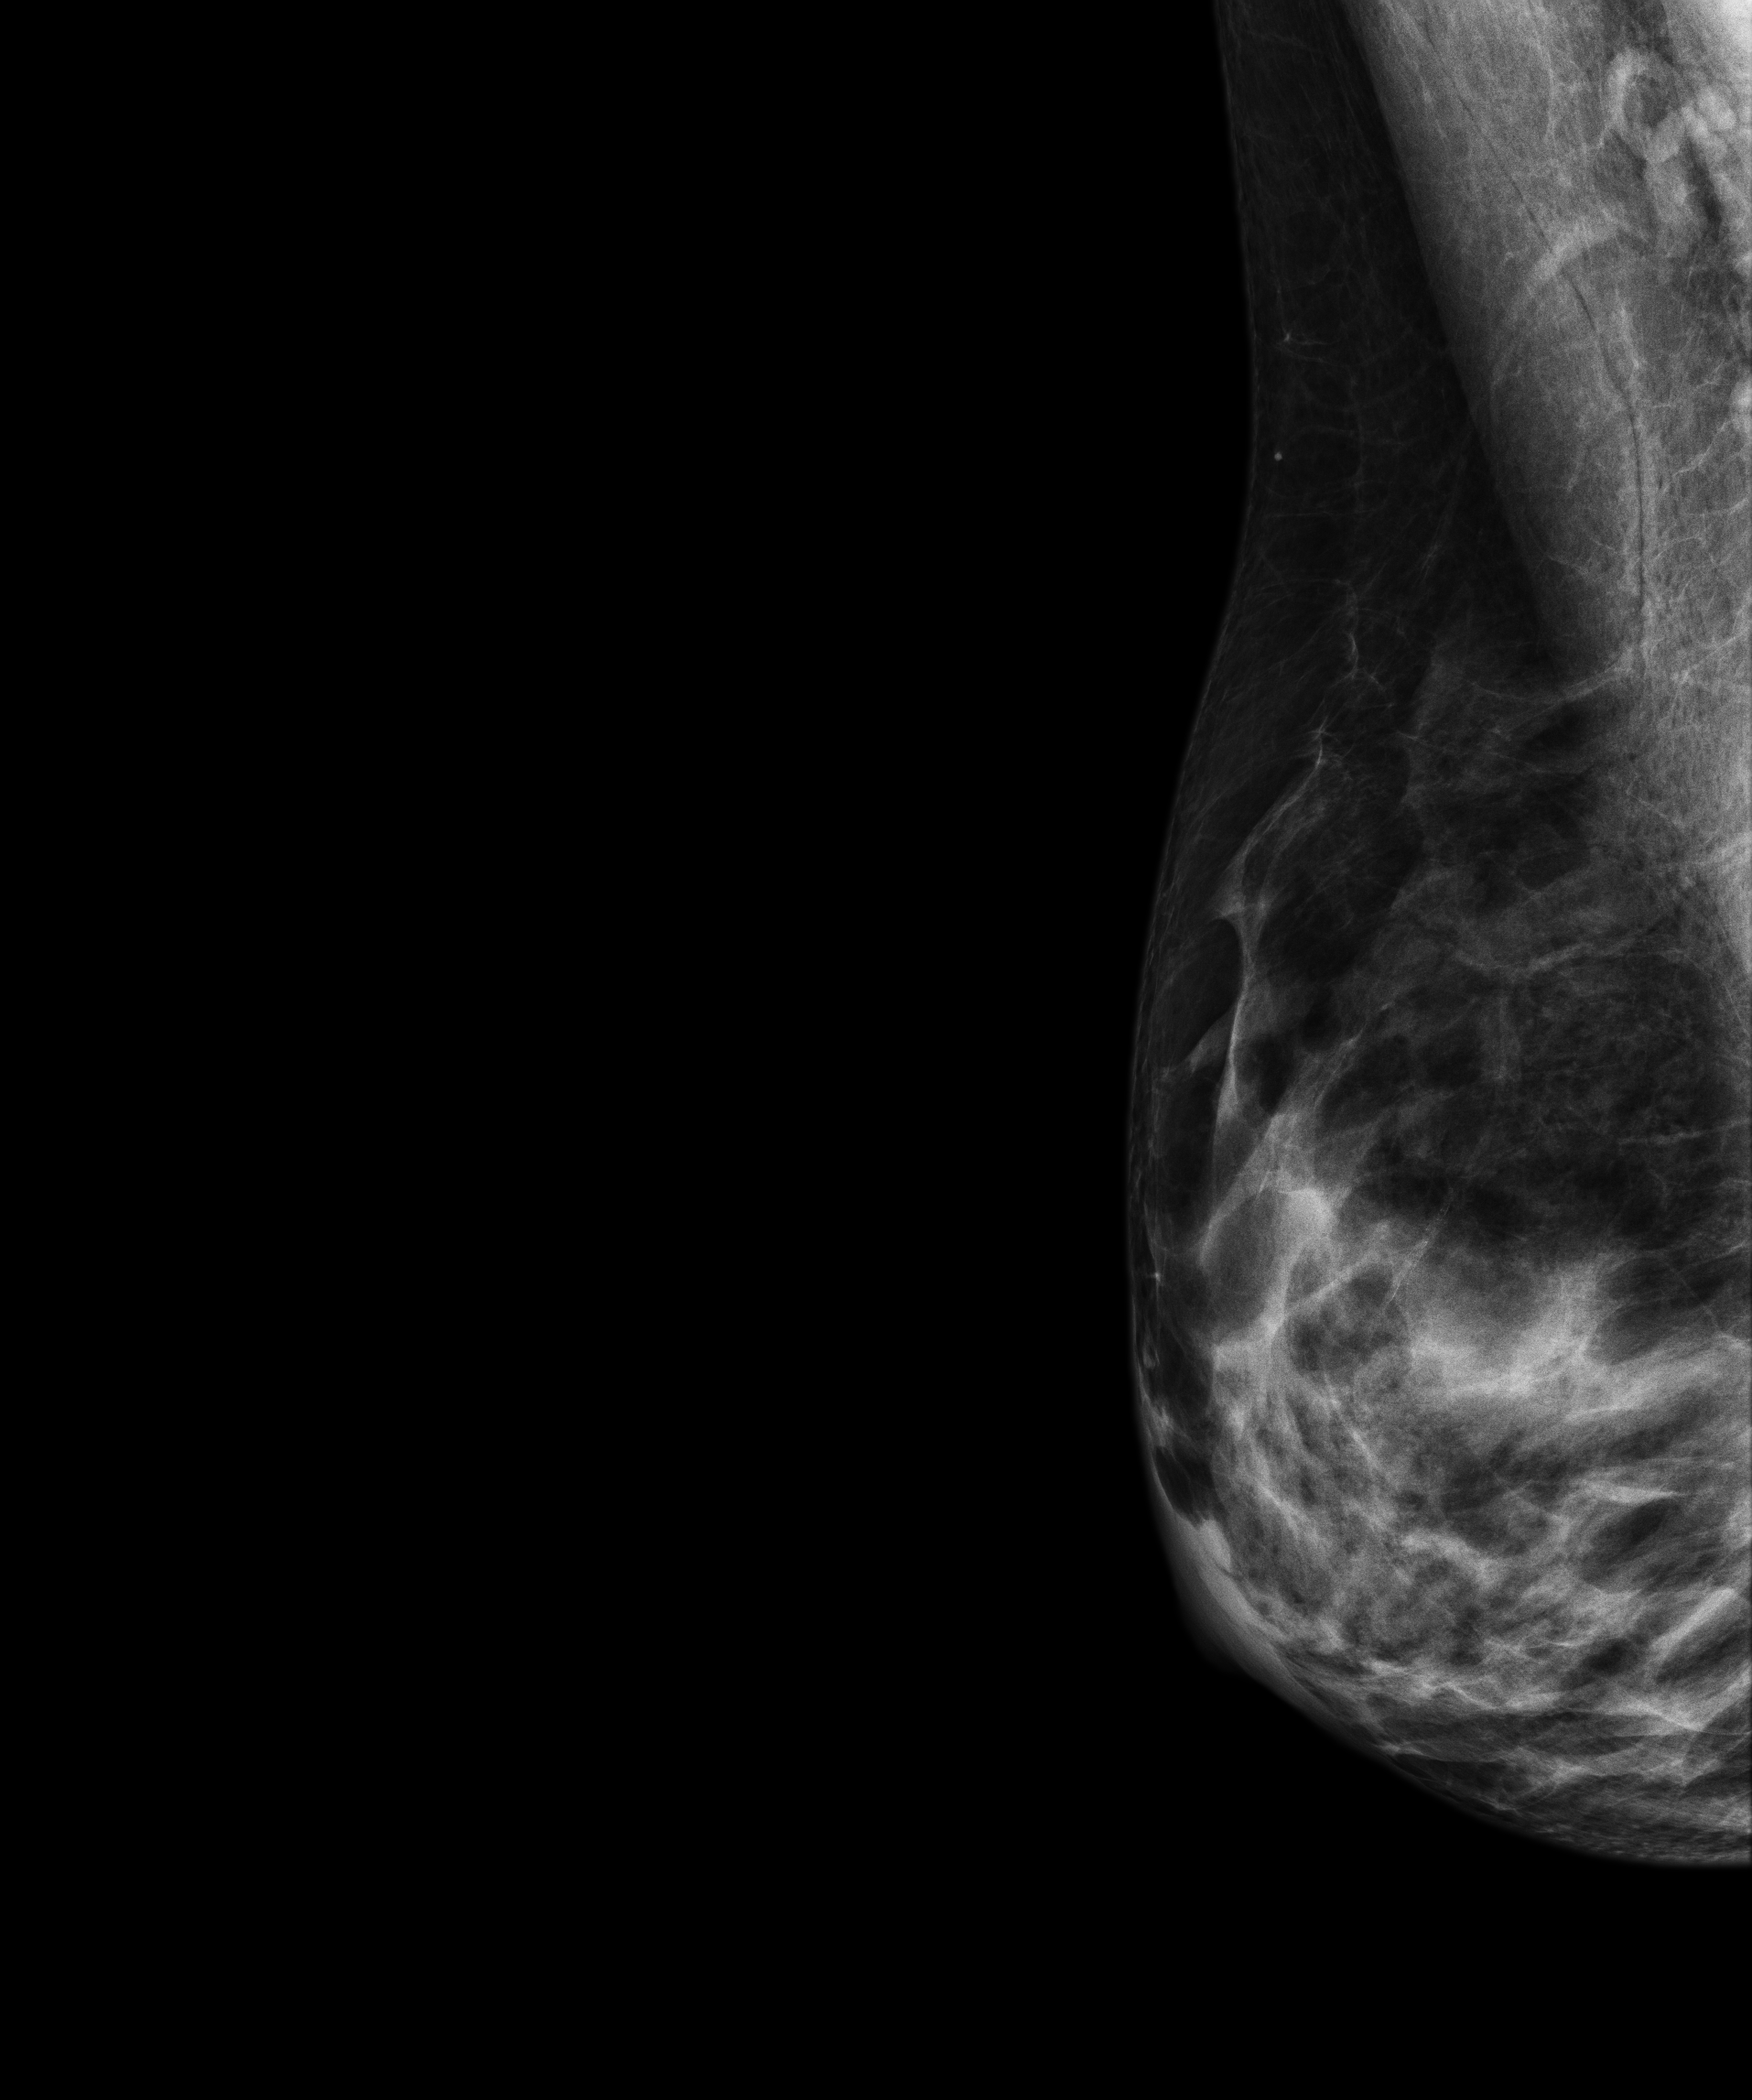
Screening examination, compressed breast thickness 48 mm. Female patient, age 67 years.
Image type: full-field digital mammogram. Breast: right. Projection: medio-lateral oblique projection.